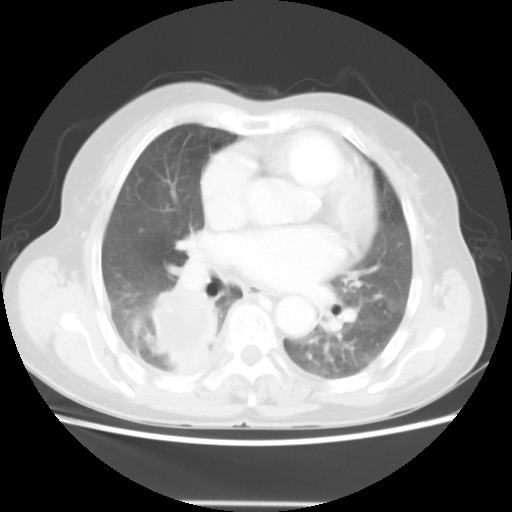
Chest CT, one axial slice. Position 26 of 52 along the scan axis. 140 kVp. Lung window (W 1500 / L -600 HU). 5 mm slice thickness. 512 × 512 image matrix. Patient: female, 67 years. From the clinical record (not read from this slice): clinical TNM (as recorded): T3 N1 M1.
Outlined on this slice (bounding box drawn by a radiologist):
- lung tumour (recorded histology: adenocarcinoma): bounding box [x1, y1, x2, y2] px = [144, 281, 220, 377]